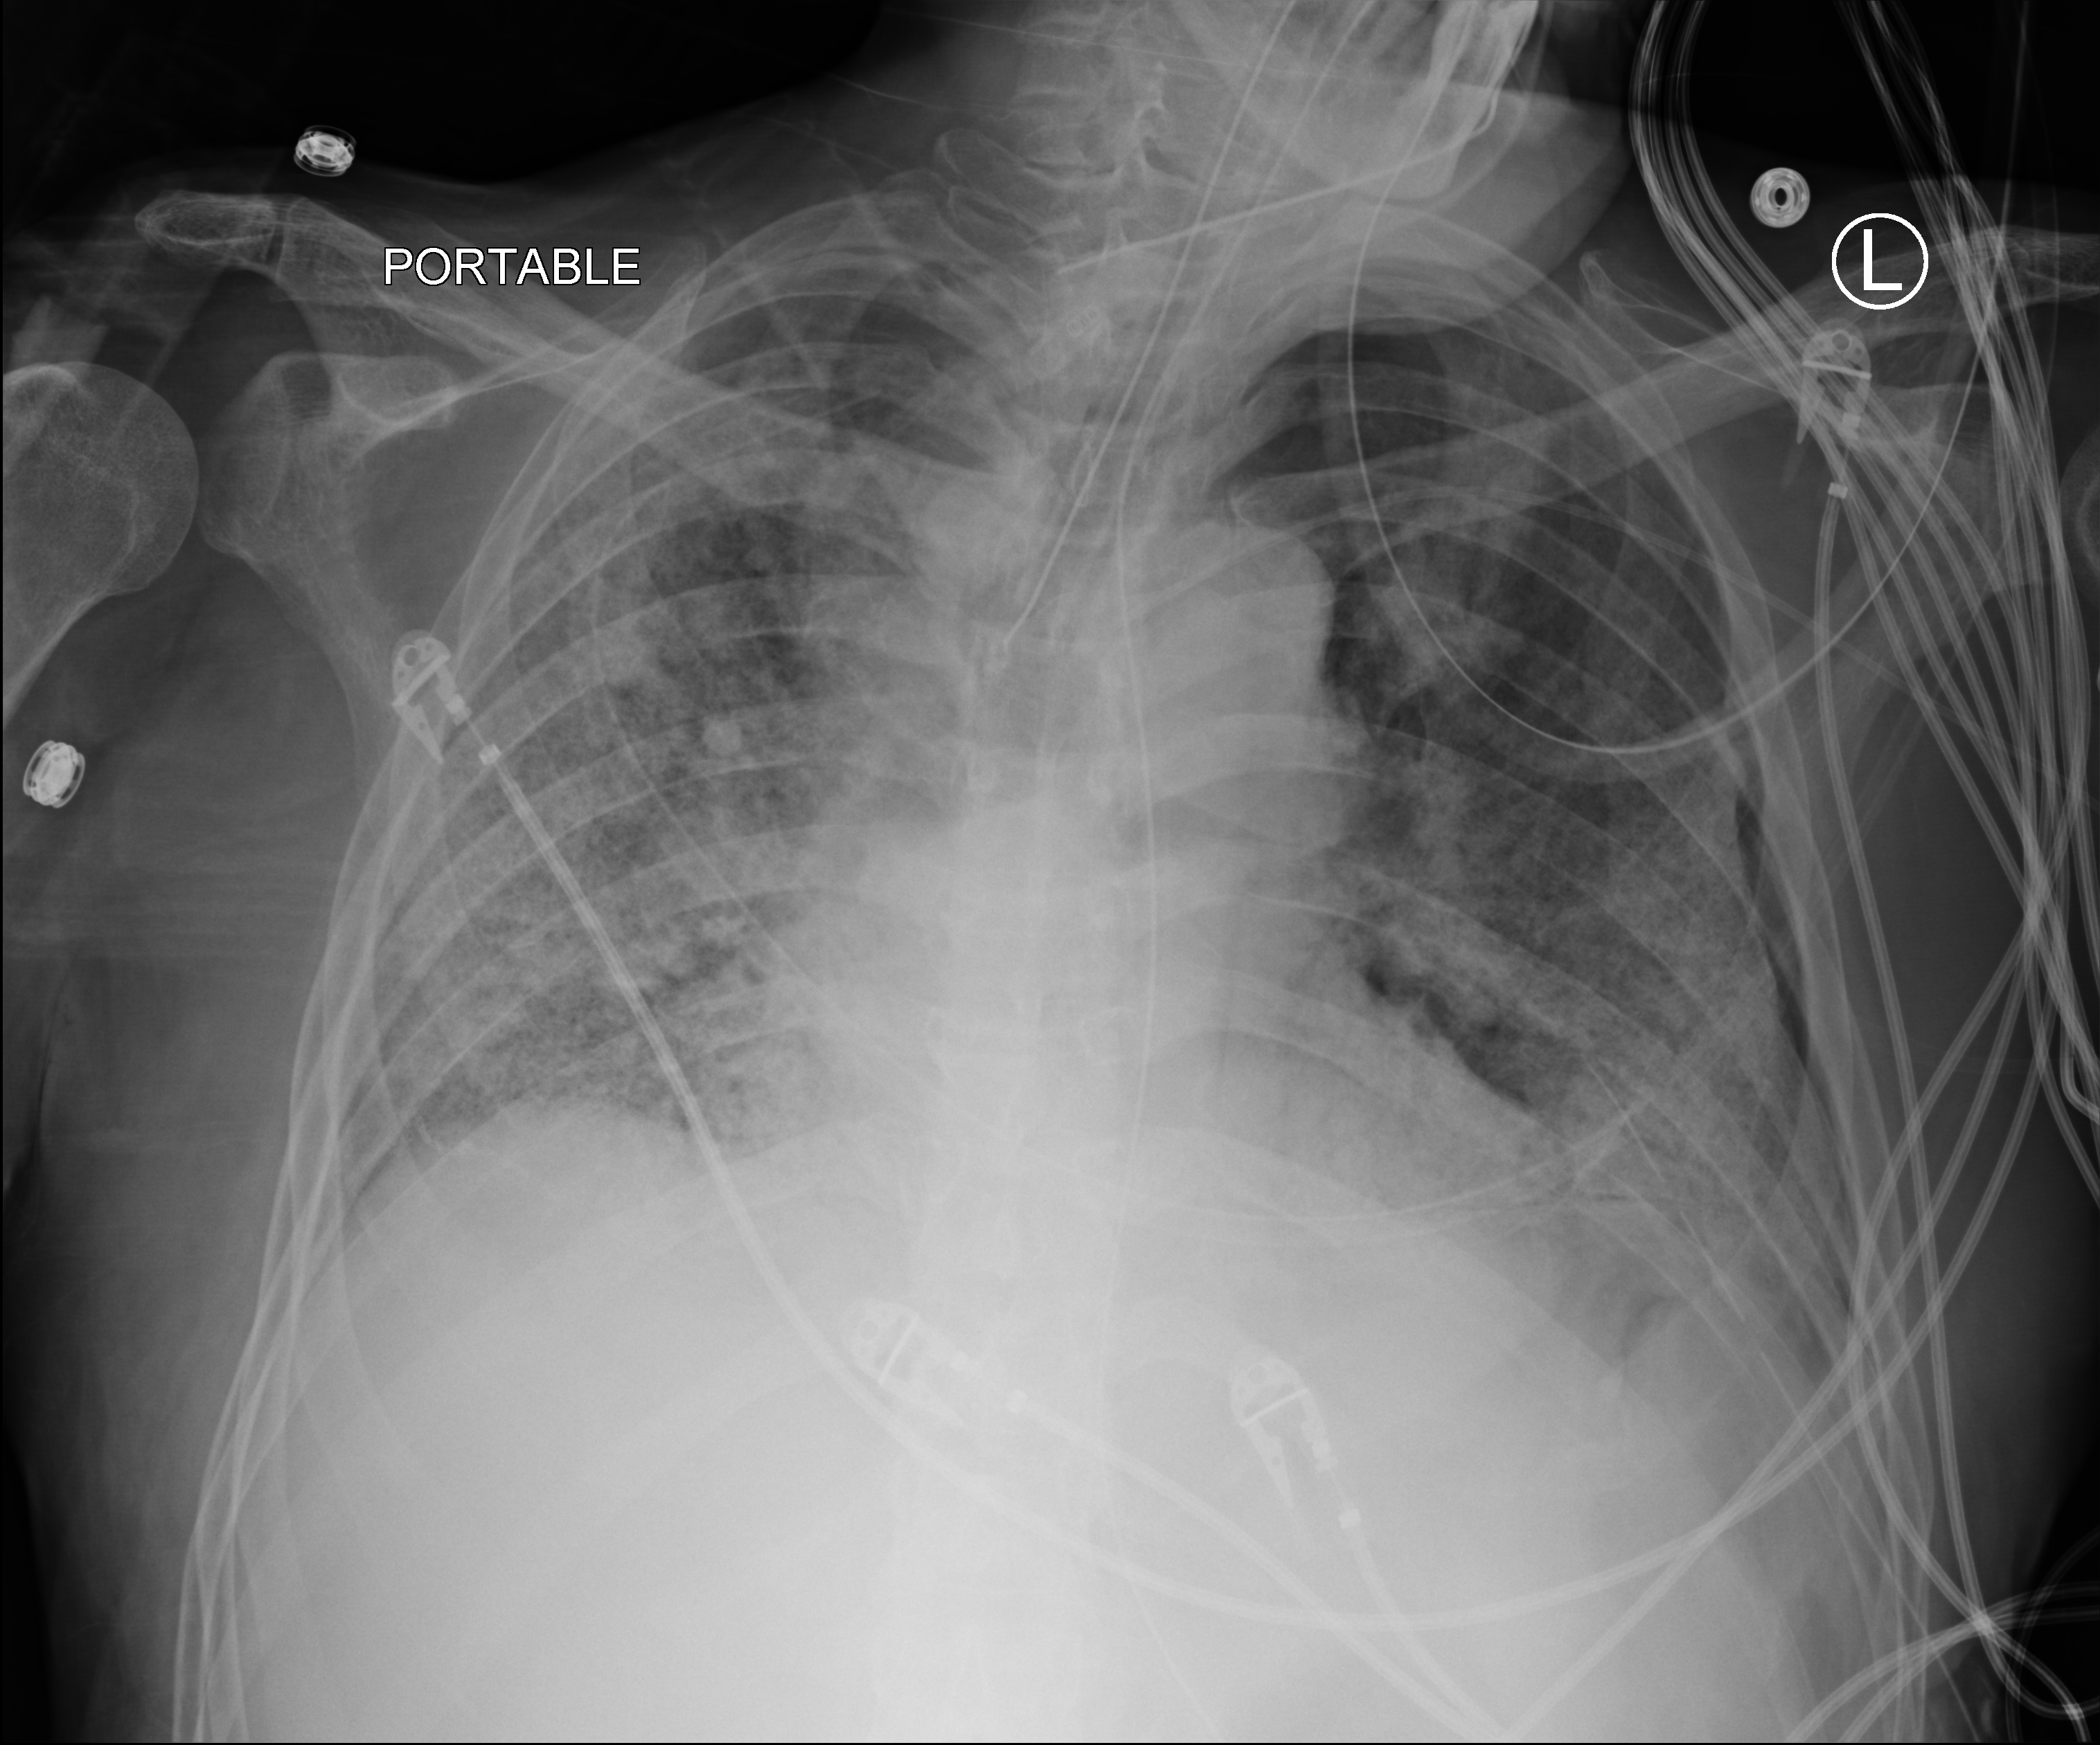
Chest X-ray (portable), anteroposterior (AP) projection. Patient hospitalised with COVID-19; male, aged 60–74 years.
Admission-level facts for this patient (not findings on this image; timing relative to this image not recorded): length of hospital stay: 54 days; admitted to intensive care during this hospital stay: yes.